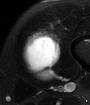
MRI of an extremity soft-tissue mass, one axial slice. Slice 18 of 65 in the series (ordered by position). T2-weighted fat-saturated. MR volume resampled by the dataset authors to the PET/CT grid (not the native acquisition matrix). 90 × 105 image matrix, field of view 88 × 103 mm. Male patient. From the clinical record (not read from this slice): histological type: mixoid liposarcoma; grade: low; site of the primary tumour: left thigh.
Structures marked on this image (expert contour drawn on MRI and transferred to this co-registered scan by the dataset authors):
- gross tumour volume (mass): bounding box (x1, y1, x2, y2) in pixels: (20, 30, 62, 81)